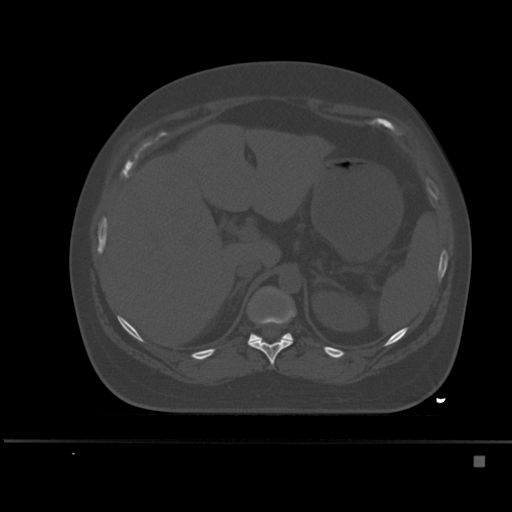
CT including the spine, one axial slice. Position 225 of 495 along the scan axis. Bone window (W 1800 / L 400 HU). 1.5 mm slice thickness. 512 × 512 image matrix, field of view 404 × 404 mm. Female patient, age 33 years. From the clinical record (not read from this slice): primary cancer: breast.
Annotated regions visible in this slice (semi-automatic segmentation, software-assisted and operator-edited):
- T11 vertebra: bounding box [x1, y1, x2, y2] px = [248, 308, 295, 366]
- T12 vertebra: [248, 333, 293, 341]